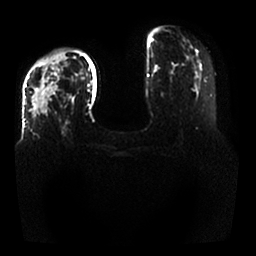
Breast MRI, one axial slice; position 12 of 25 along the scan axis; diffusion-weighted series; image 2 of 4 stored at this slice position (different b-values; order by instance number); 1.5 T; 4 mm slice thickness; 256 × 256 image matrix, field of view 350 × 350 mm. Female patient.
Outlined on this slice (manually delineated by an expert):
- tumour on diffusion-weighted imaging: box from (x=32, y=54) to (x=65, y=116) px